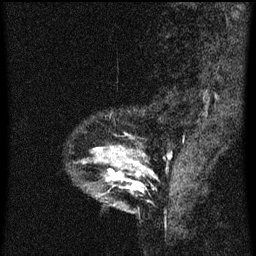
Breast MRI (dynamic contrast-enhanced), one sagittal slice; dynamic contrast-enhanced series, image 2 of 3 at this slice position (ordered by acquisition); 1.5 T; TE 4.2 ms, TR 8 ms; 2 mm slice thickness; 256 × 256 image matrix, field of view 180 × 180 mm. Patient: female, 33 years.
Structures marked on this image (semi-automatic segmentation, software-assisted and operator-edited):
- analysis volume of interest (the breast-tissue region the enhancement analysis was run in; not a lesion): box from (x=91, y=148) to (x=144, y=213) px
- tumour enhancement mask (voxels above the 70 % enhancement threshold inside the analysis volume of interest): (x=109, y=152)–(x=141, y=185)